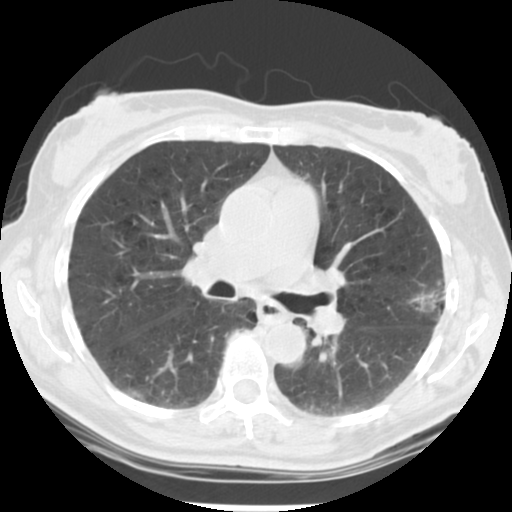
Chest CT (low-dose screening protocol), one axial image, second screening round (one year after baseline), lung window (W 1500 / L -600 HU), standard (soft-tissue) reconstruction kernel (STANDARD), 512 × 512 image matrix. Female, age 61 years at enrolment. Current smoker at enrolment.
Lesion marked by an expert reader, box from (x=403, y=273) to (x=464, y=333) px. Reader record for this screening exam (exam-level; its link to the box is not recorded): non-calcified nodule or mass ≥4 mm, left upper lobe, 15 × 15 mm, poorly defined margins, mixed attenuation, pre-existing on the prior screen: no.